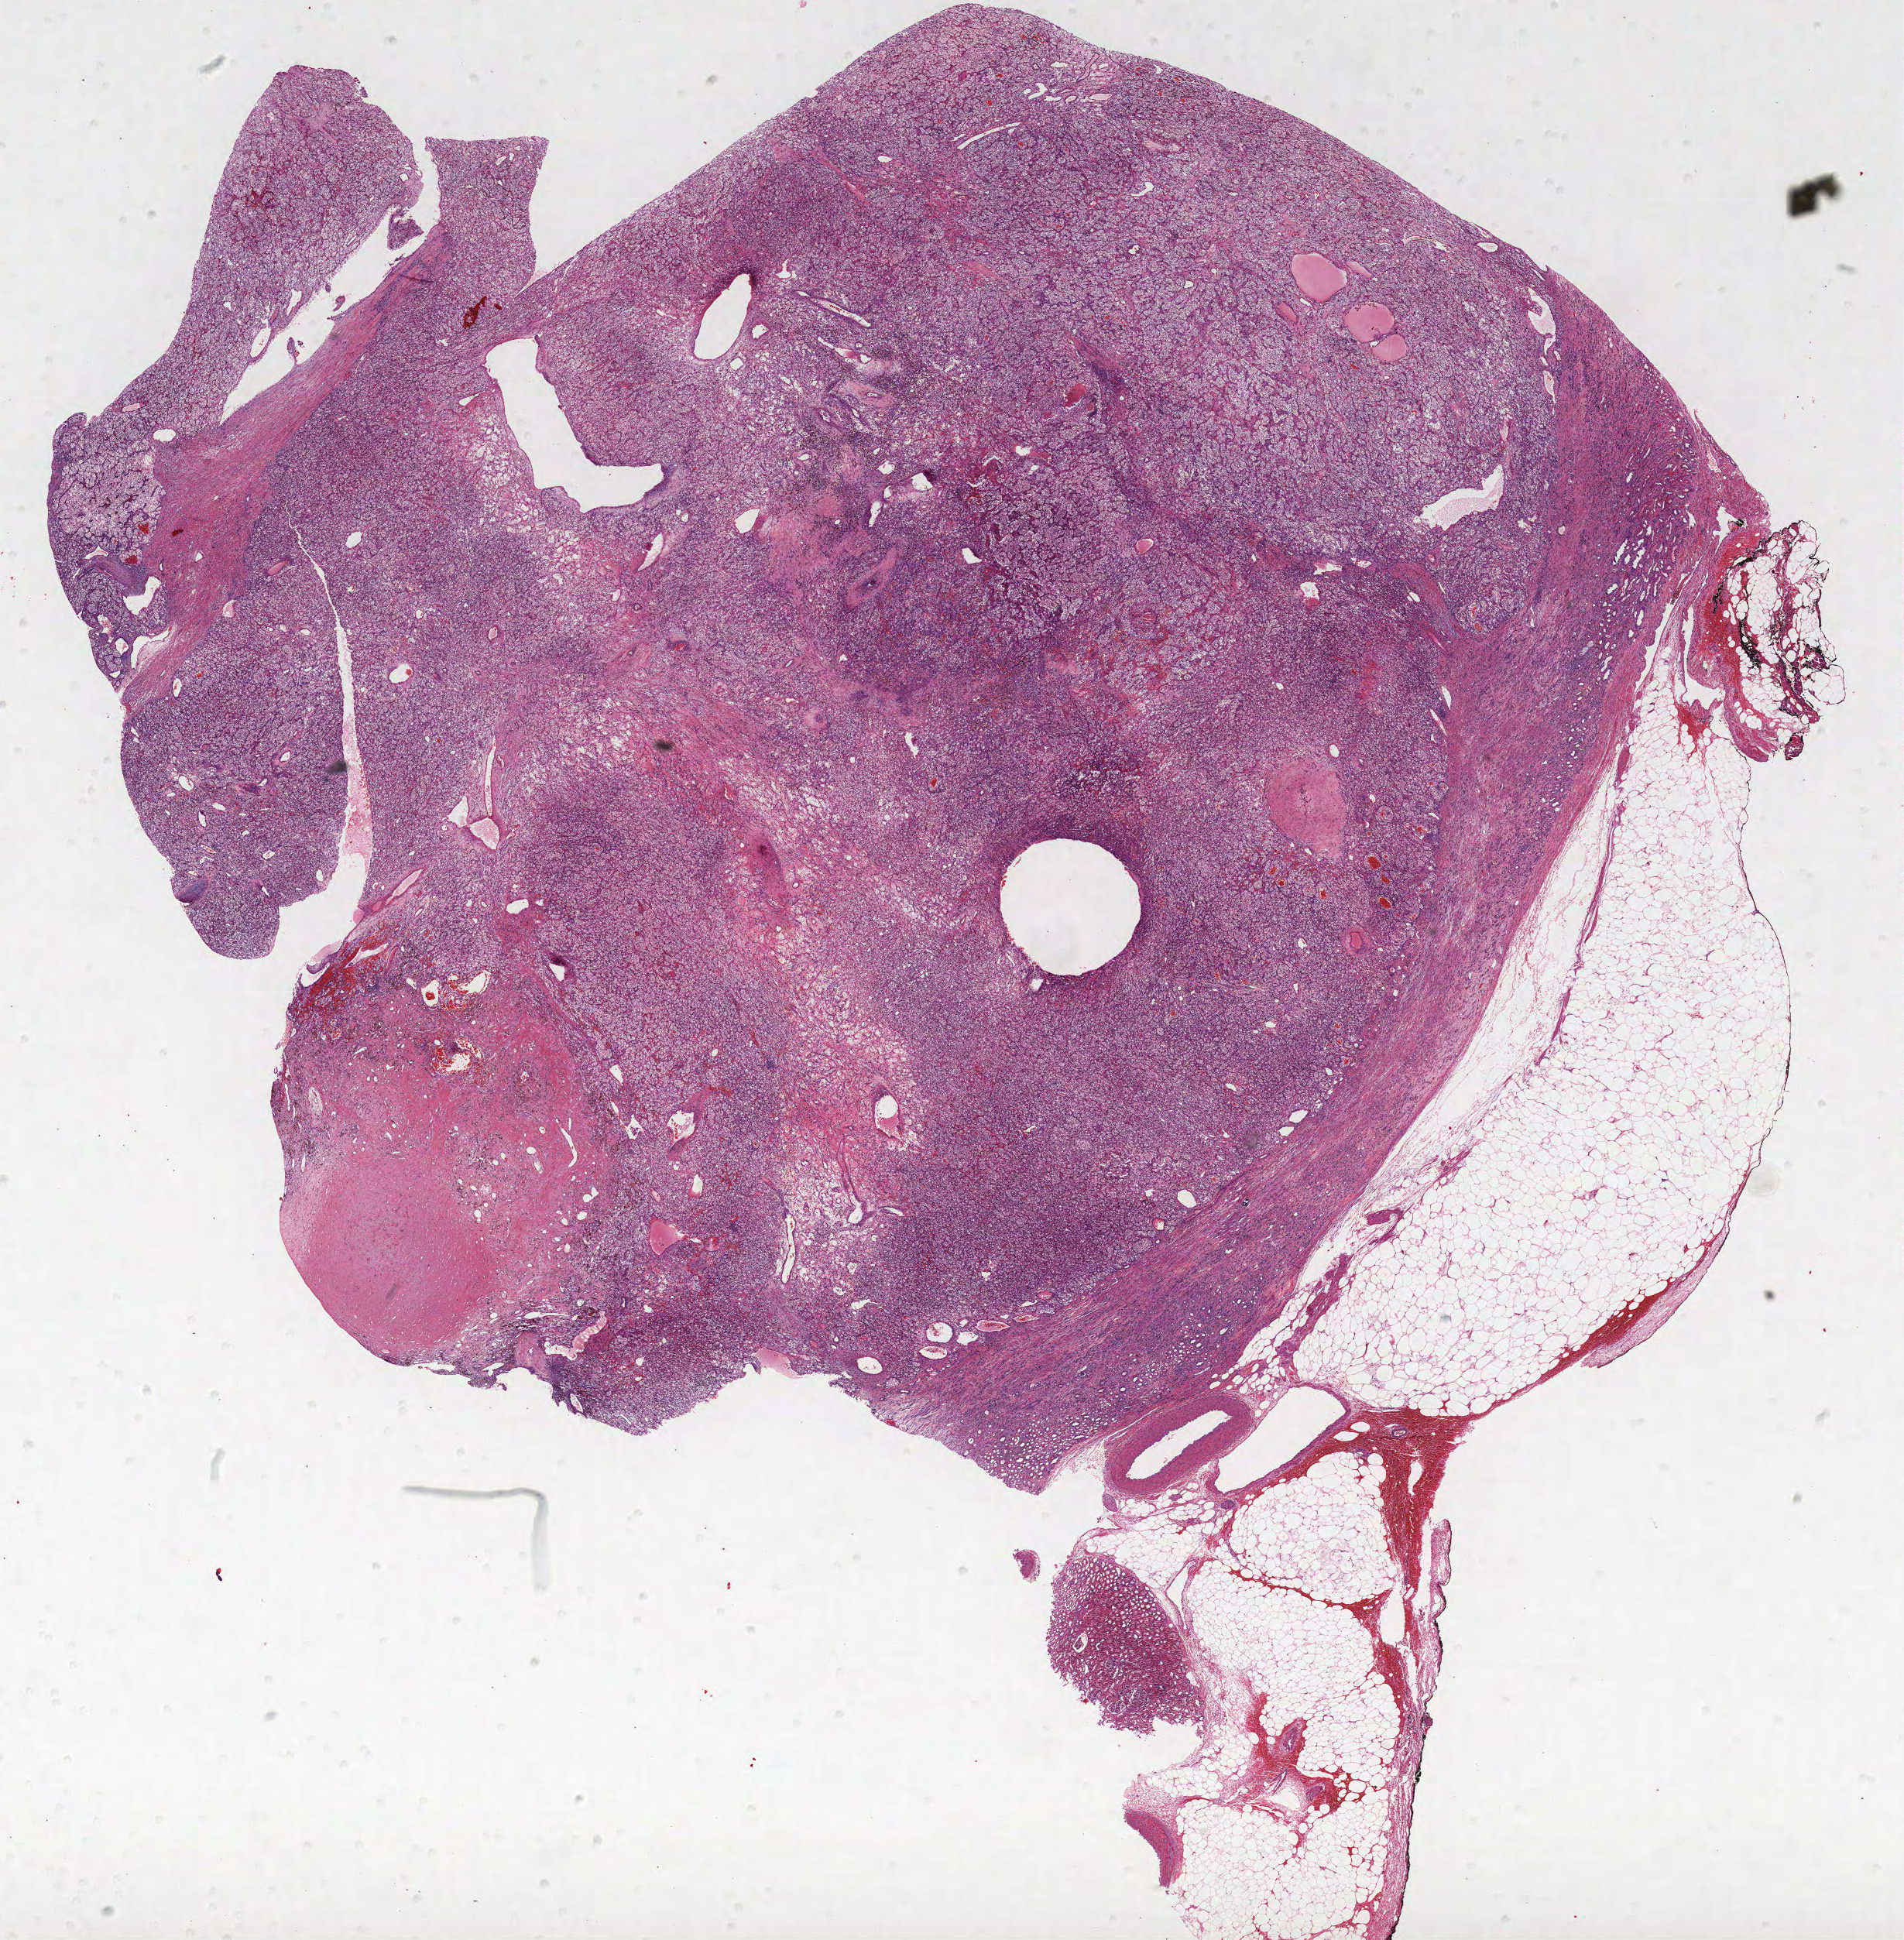
Digitized H&E tissue section (whole slide), whole scanned area (about 19.7 x 20.0 mm, slide scanned at 40x) shown as a low-resolution overview; formalin-fixed paraffin-embedded (FFPE) diagnostic section; primary tumour sample from the kidney. Male patient; age at initial diagnosis 40 years. Histologic grade: G3 (poorly differentiated).
• histologic diagnosis: Clear cell adenocarcinoma, NOS
• AJCC pathologic stage: I
• laterality: right